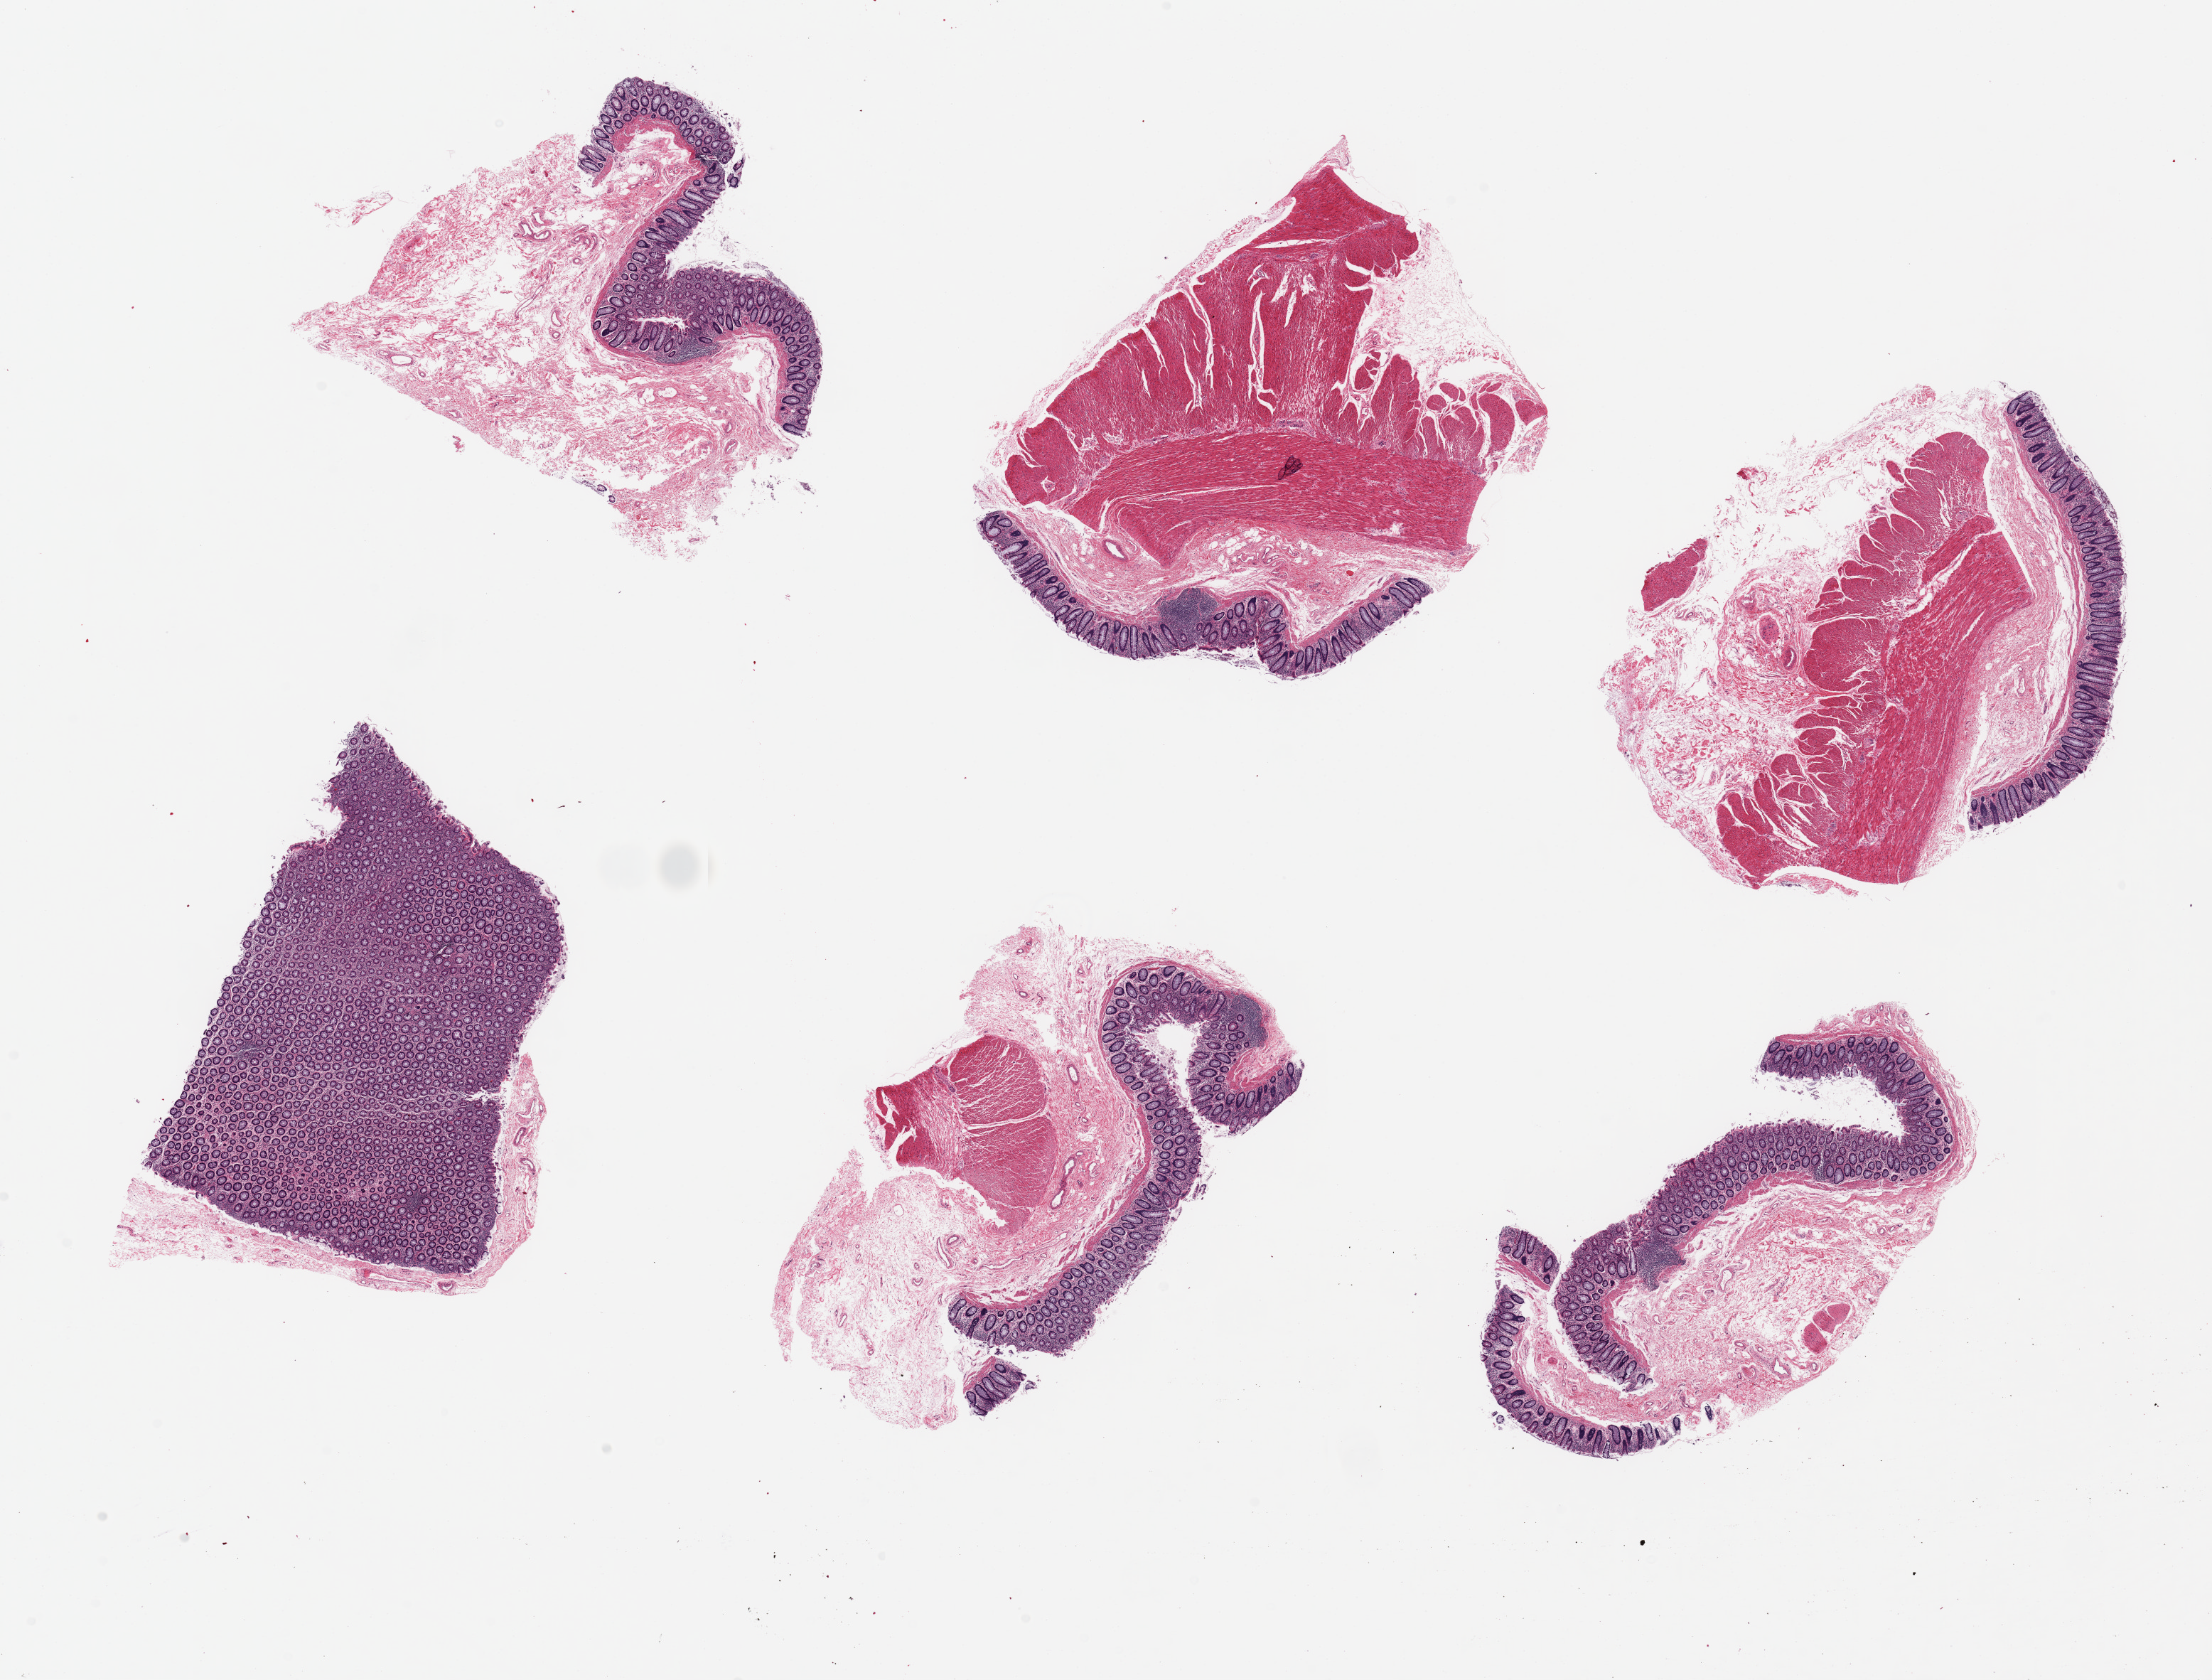
Whole-slide image, hematoxylin and eosin (H&E) stain, brightfield, low-resolution overview of the scanned area, about 24.6 x 18.7 mm (slide scanned at 20x), PAXgene-fixed paraffin-embedded (PFPE) section, section of sigmoid colon (target tissue), donor tissue sample. Donor sex: male.
Reviewer comment on this tissue sample: 6 pieces ~6x3mm. Mucosa well preserved, ~15-20% thickness.